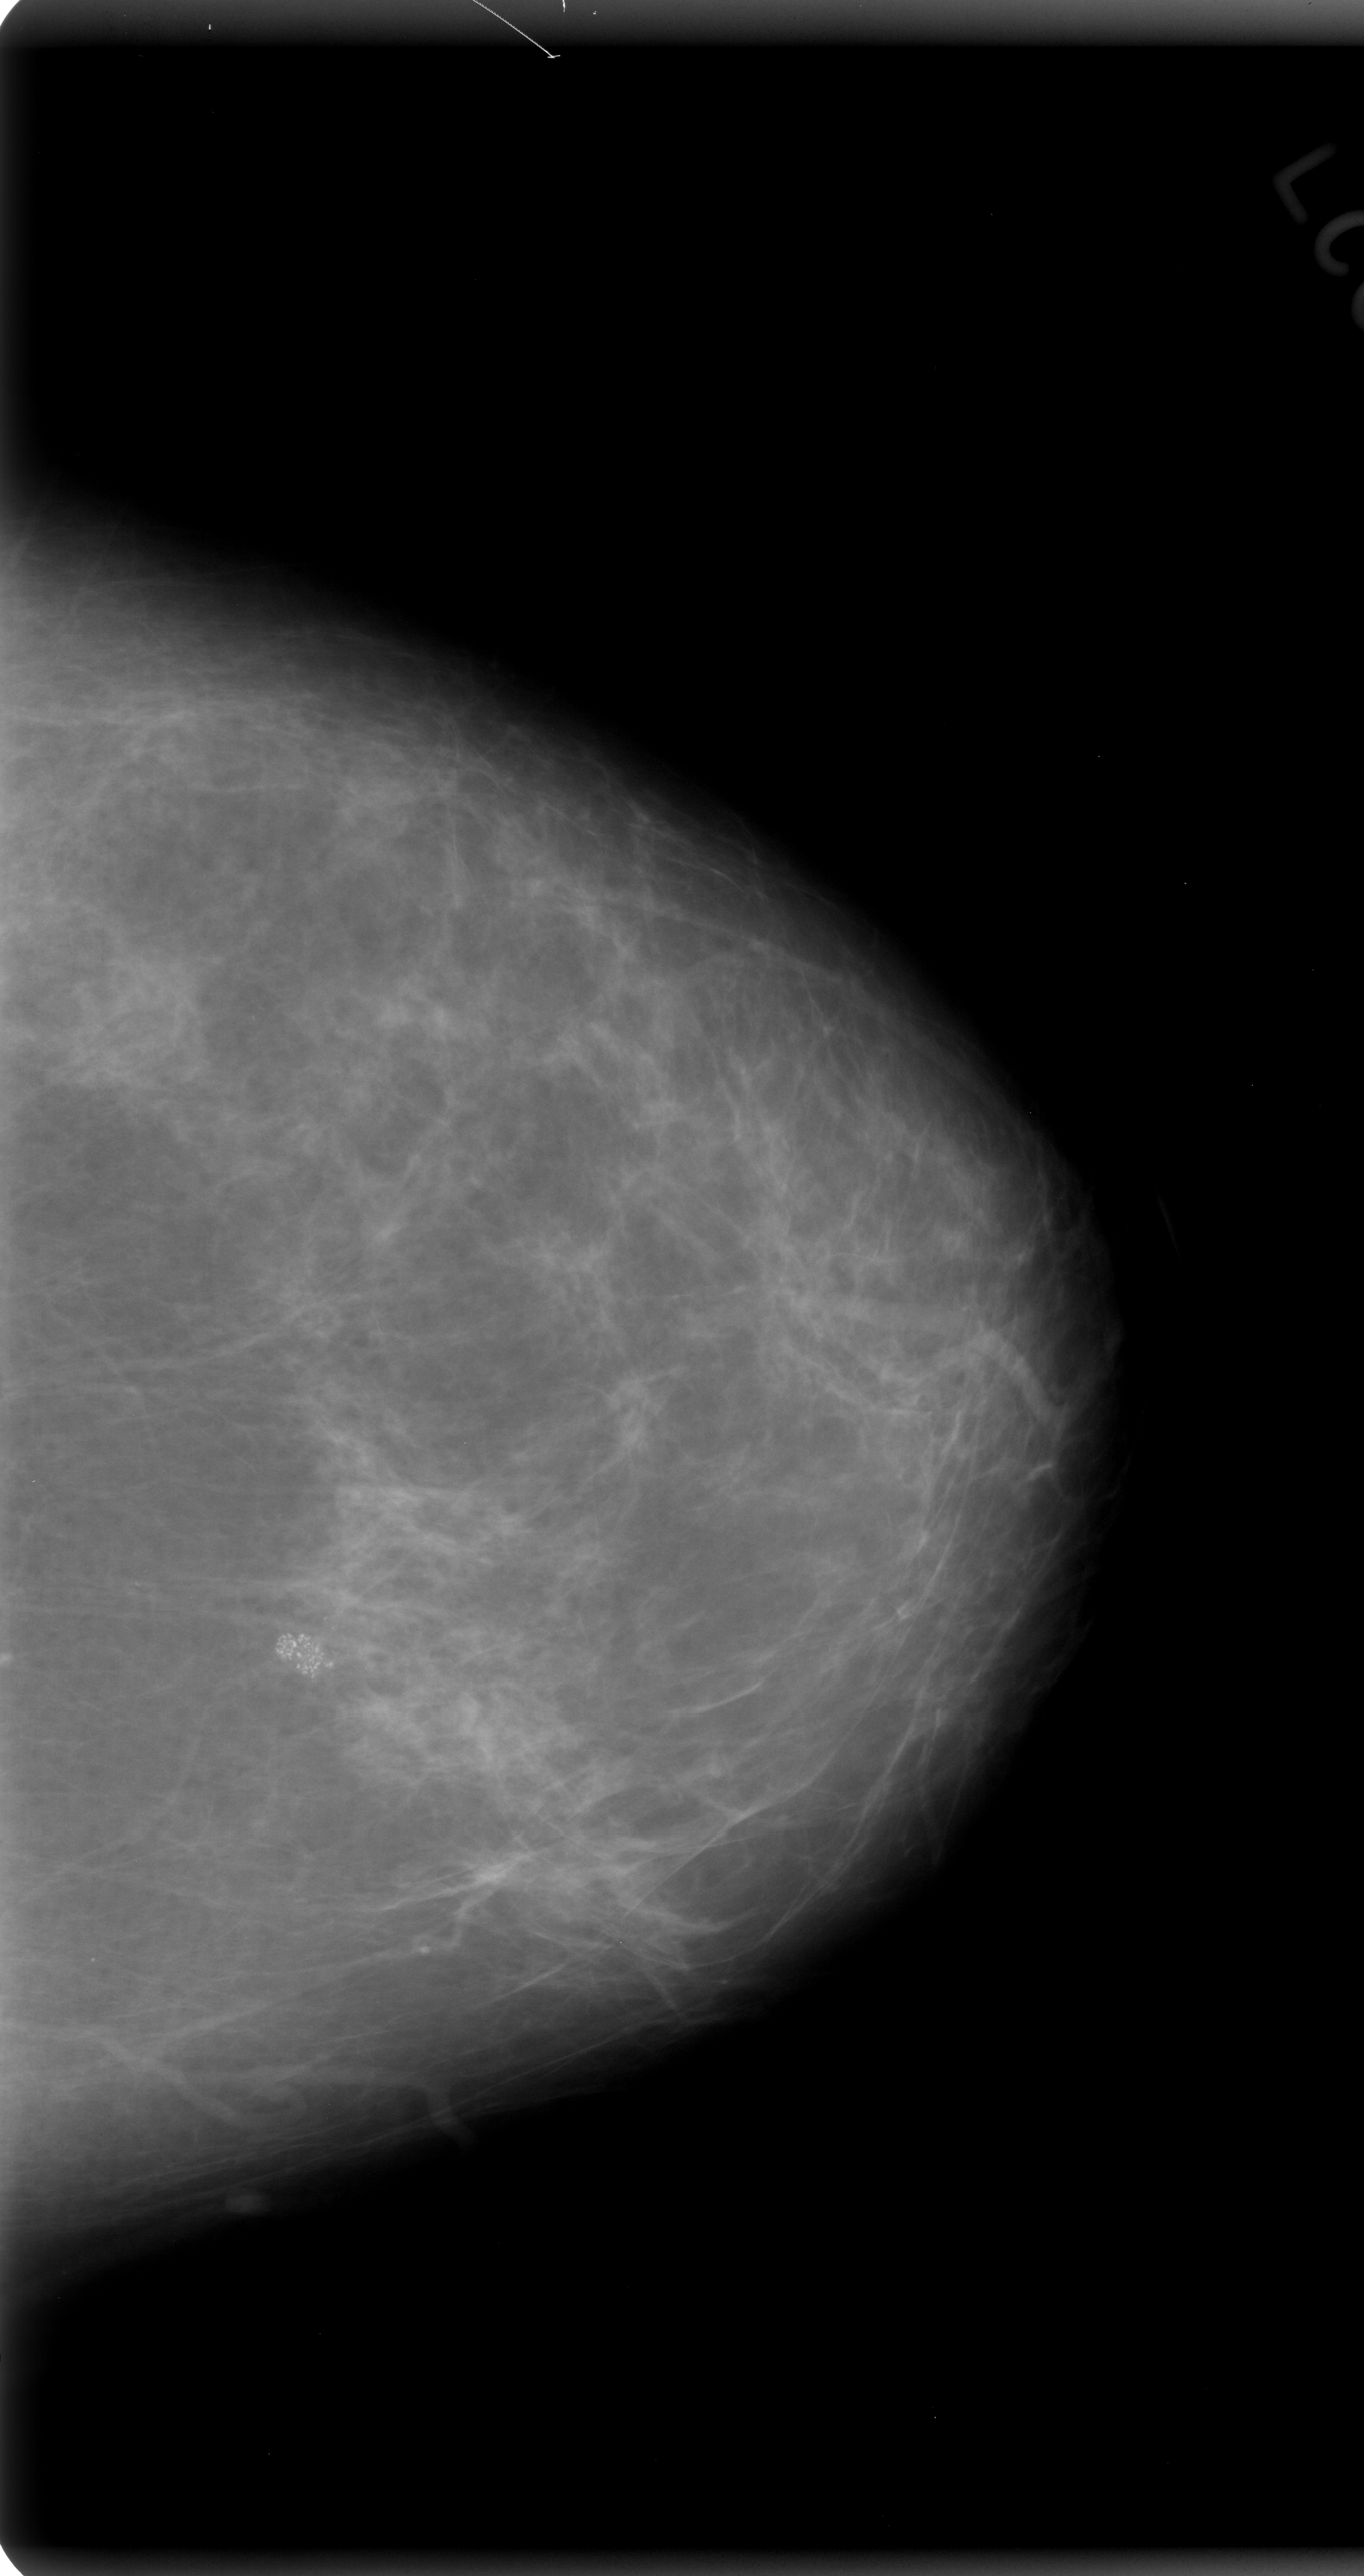
Mammogram (digitized film). Left breast. CC view. BI-RADS breast density category 2 (scale 1–4). 1364 × 2576 image matrix.
Expert-marked regions of interest on this image (one box per marked abnormality):
- calcifications, morphology pleomorphic, distribution clustered; BI-RADS assessment category 5; pathology (as recorded): malignant: bounding box [x1, y1, x2, y2] px = [207, 1568, 385, 1777]